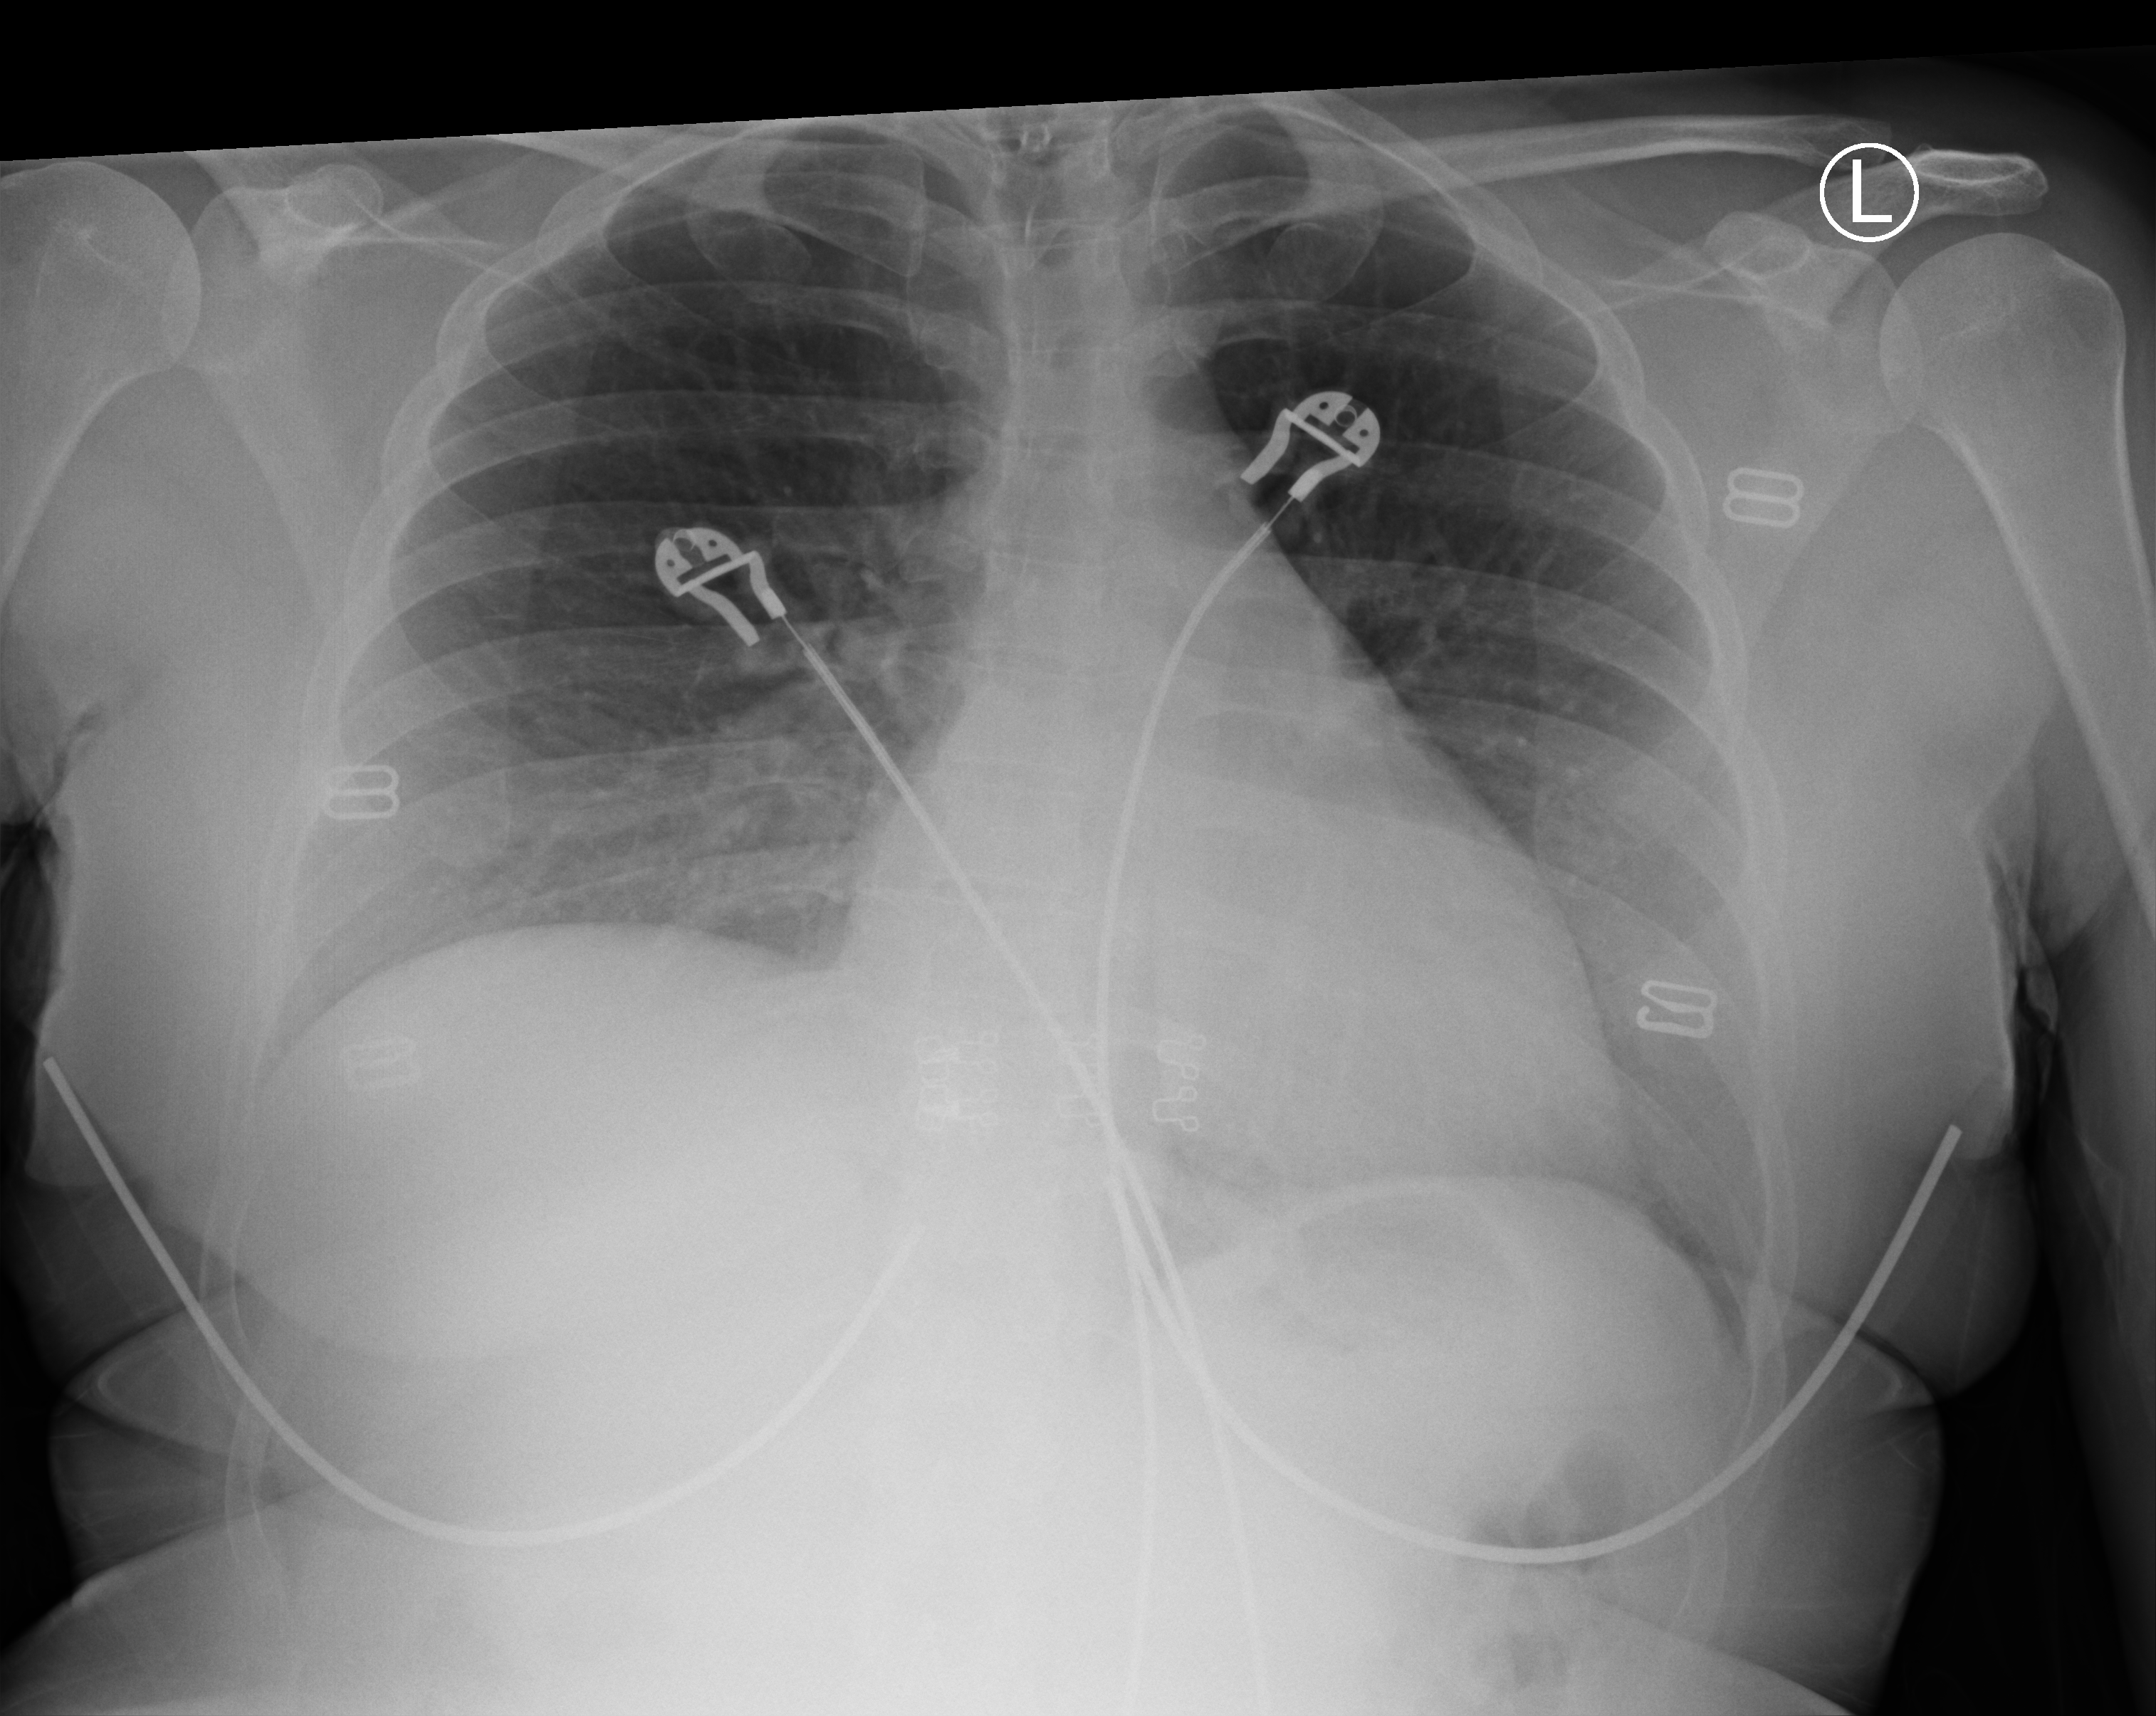
Chest X-ray (portable); anteroposterior (AP) projection. Female patient hospitalised with COVID-19, age 18–59 years.
Admission-level facts for this patient (not findings on this image; timing relative to this image not recorded):
- mechanically ventilated during this hospital stay: no